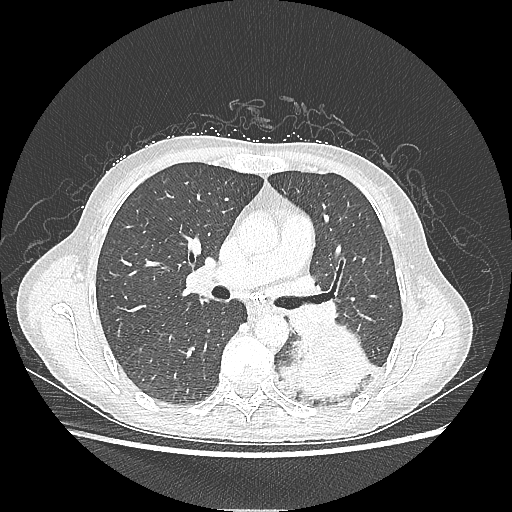
Chest CT, one axial slice; slice 128 of 220 in the series (ordered by position); reconstruction kernel LUNG; 80 kVp; lung window (W 1500 / L -600 HU); 1.25 mm slice thickness; 512 × 512 image matrix, field of view 360 × 360 mm. Patient: female, 53 years. Case-level facts recorded for this patient, not image findings: clinical TNM (as recorded): T3 N0 M0.
Structures marked on this image (bounding box drawn by a radiologist):
- lung tumour (recorded histology: adenocarcinoma): box from (x=279, y=330) to (x=371, y=403) px